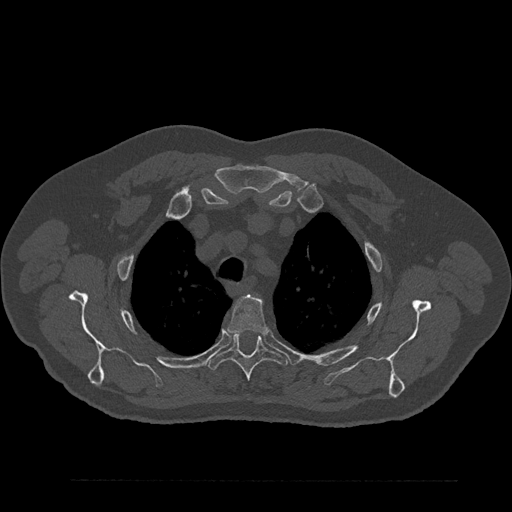
CT including the spine, one axial slice; position 660 of 797 along the scan axis; 120 kVp; bone window (W 1800 / L 400 HU); 0.5 mm slice thickness; 512 × 512 image matrix, field of view 430 × 430 mm. Male patient, age 61 years. Case-level facts recorded for this patient, not image findings: primary cancer: prostate.
Structures marked on this image (semi-automatically segmented with operator editing):
- T3 vertebra: bounding box <228,296,267,335> (left, top, right, bottom; pixels)
- T4 vertebra: <206,332,288,381>